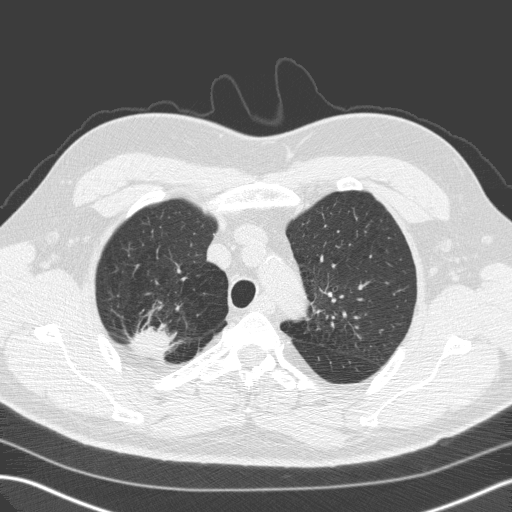
Low-dose screening chest CT, one axial slice; slice 123 of 149 in the series (ordered by position); 120 kVp; lung window (W 1500 / L -600 HU); 2 mm slice thickness; 512 × 512 image matrix, field of view 357 × 357 mm.
Structures marked on this image (expert manual segmentation):
- lesion 1 (tumor, upper lobe of right lung): bounding box (x1, y1, x2, y2) in pixels: (129, 329, 172, 356)